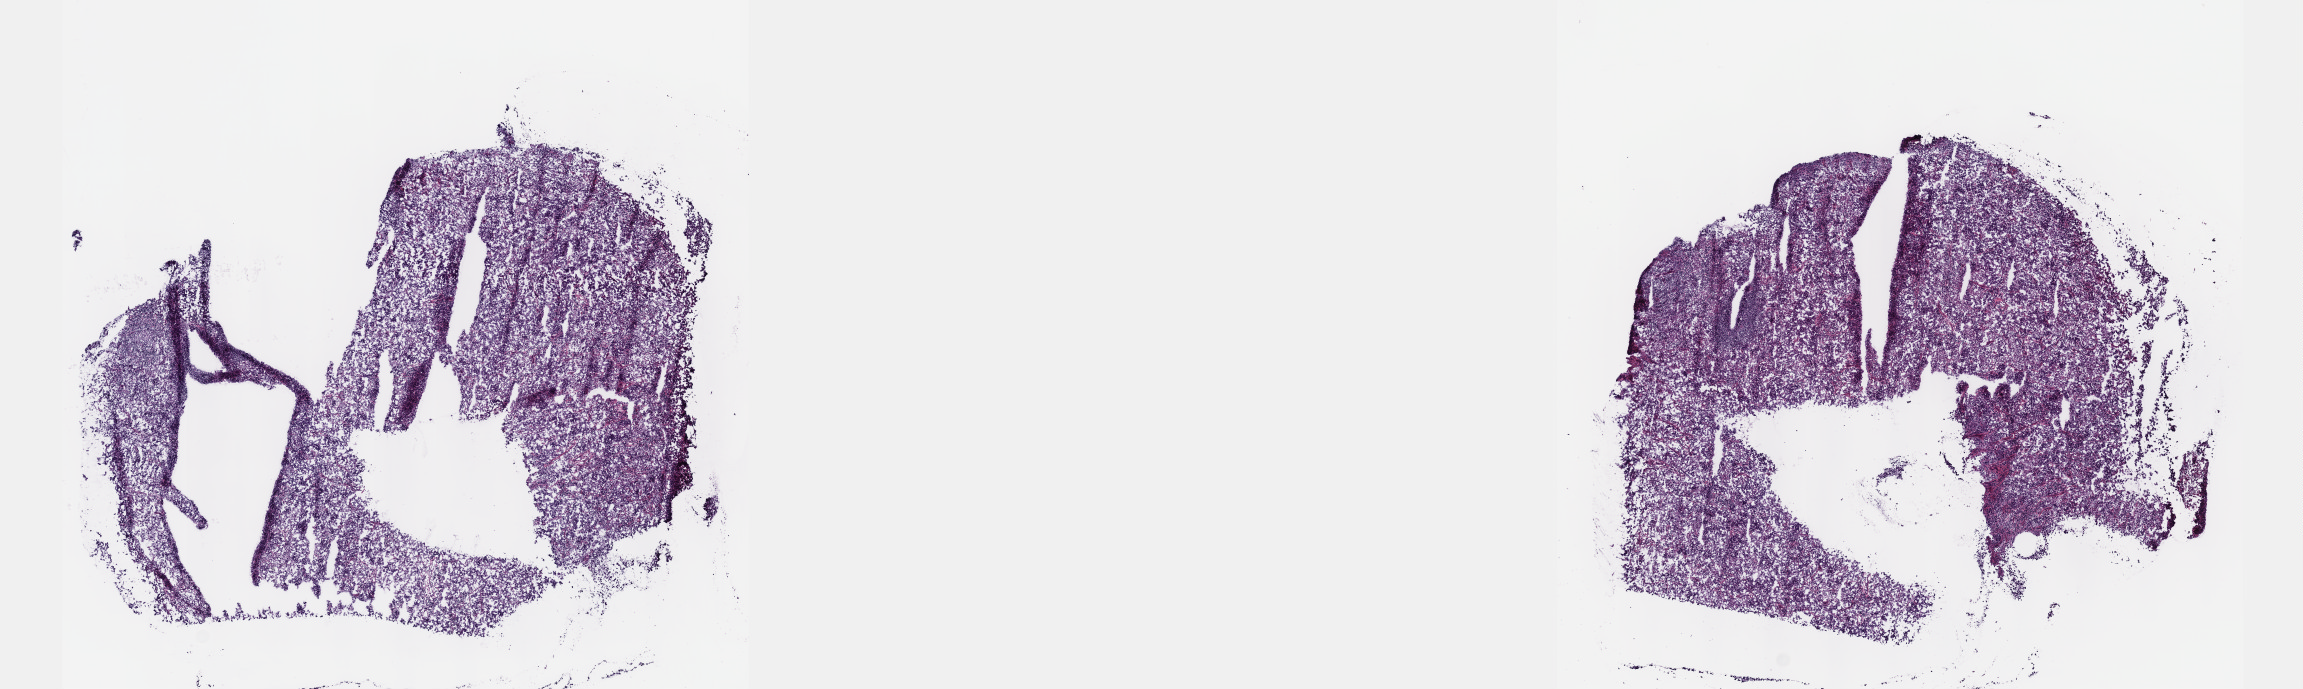
Whole-slide histology image, Hematoxylin and eosin (H&E) stained — shown as a low-resolution overview of the whole scanned area (about 18.6 x 5.6 mm, from a 40x scan); frozen section from the top of the tissue portion; primary tumour sample from the testis. Male, age 39 years at initial diagnosis. Composition of this section per pathologist review: tumour cells 100%, tumour nuclei 70%, normal cells 0%, stromal cells 0%, necrosis 0%. Infiltration values recorded for this section: lymphocyte infiltration 5%, monocyte infiltration 0%, neutrophil infiltration 0%.
Laterality: bilateral. Pathologic diagnosis: Seminoma, NOS. AJCC pathologic stage: IA (7th edition).